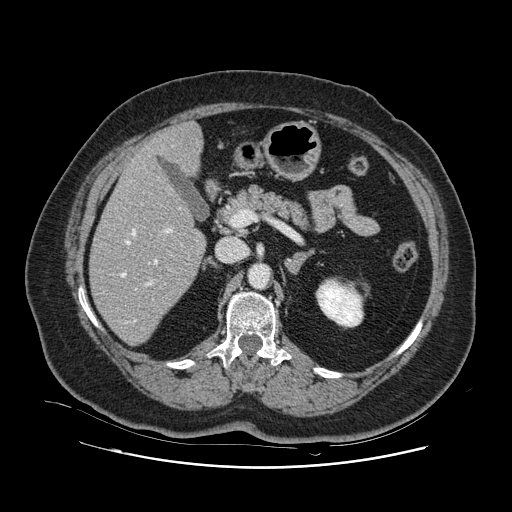
Contrast-enhanced abdominal CT, one axial slice. Slice 54 of 132 in the series (ordered by position). Intravenous contrast given. Soft-tissue window (W 400 / L 40 HU). 512 × 512 image matrix, field of view 391 × 391 mm. Female patient, age 73 years. From the clinical record (not read from this slice): diagnosis: colorectal cancer liver metastases, imaged before liver resection; multiple liver metastases: no; largest metastasis: 7 cm; disease in both lobes: no.
Structures marked on this image (outlined manually by an expert reader):
- hepatic veins: bounding box <121,146,183,321> (left, top, right, bottom; pixels)
- liver: <90,124,205,344>
- planned liver remnant (the part of the liver to remain after resection): <90,148,205,345>
- portal vein (with intrahepatic branches): <146,228,172,286>